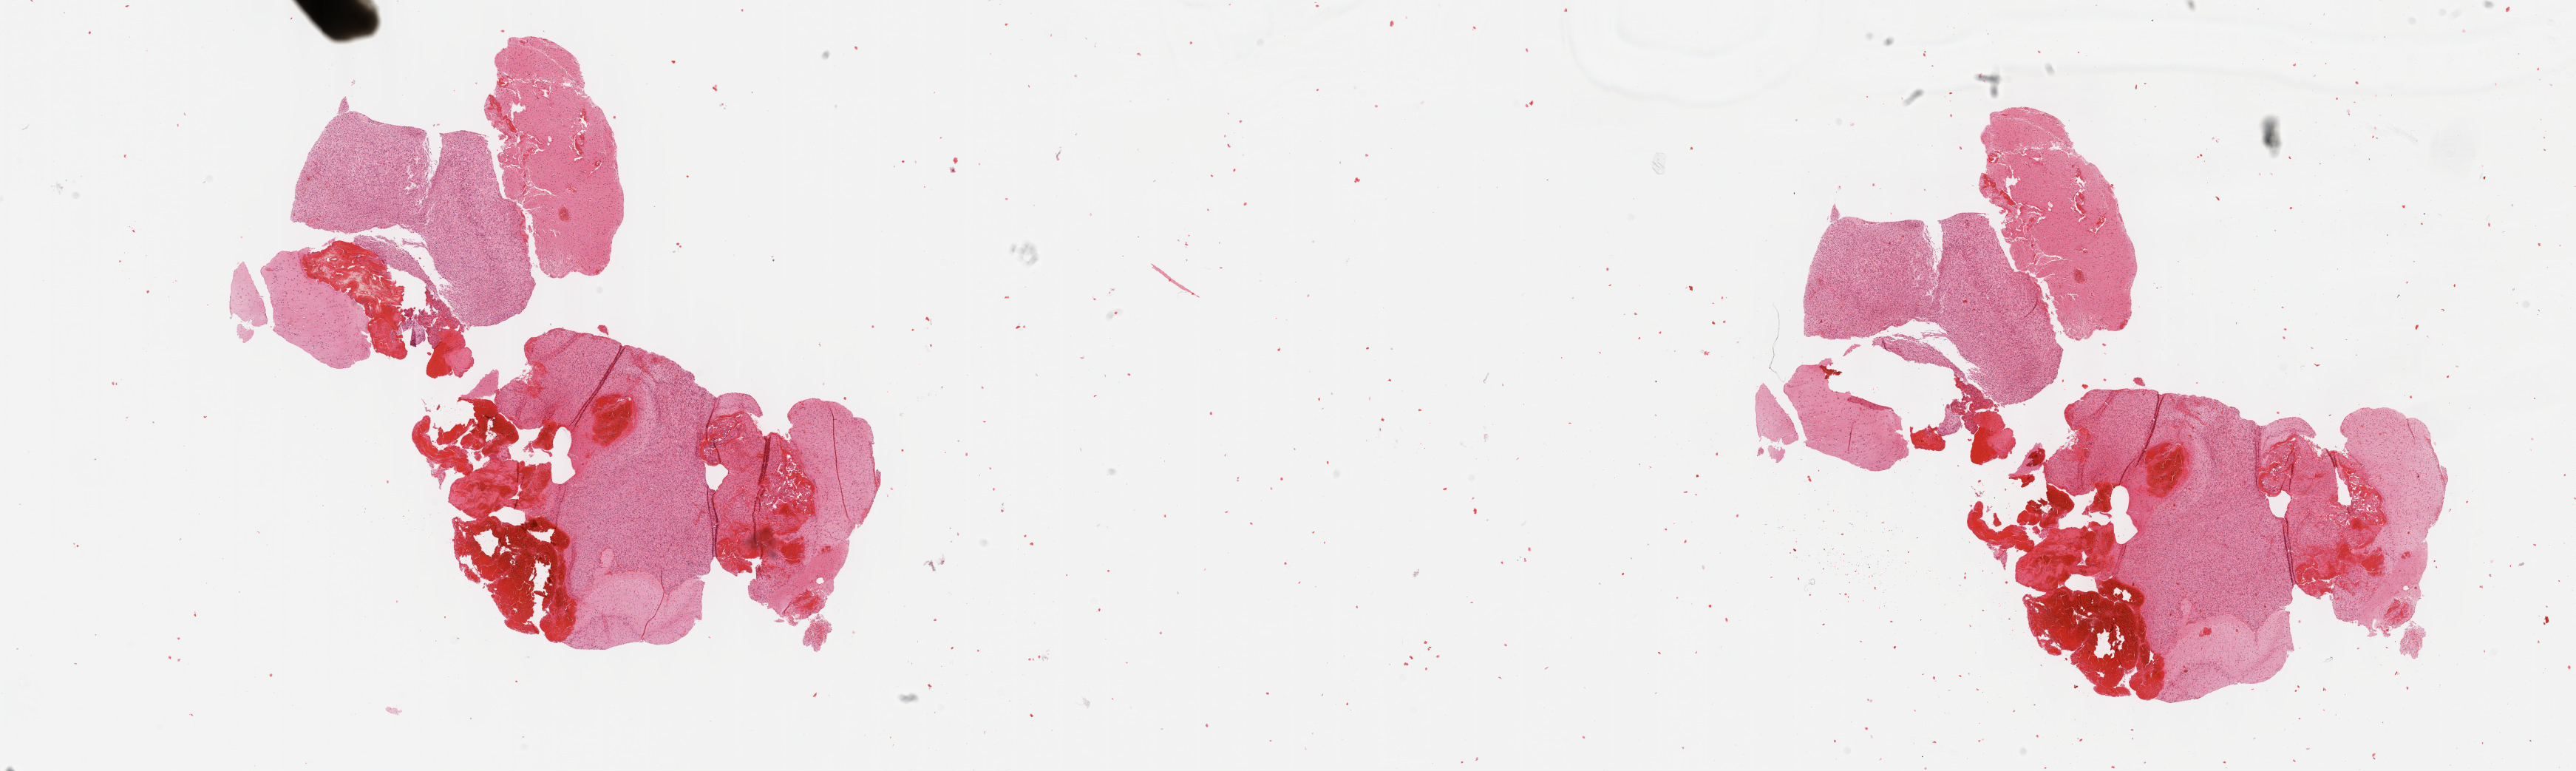
Digitized H&E tissue section (whole slide), shown as a low-resolution overview of the whole scanned area (about 28.2 x 8.4 mm). Formalin-fixed paraffin-embedded (FFPE) diagnostic section. Primary tumour sample from the brain. Patient: male, age at initial diagnosis 57 years. Histologic grade: G3 (poorly differentiated).
Pathologic diagnosis: Astrocytoma, anaplastic.